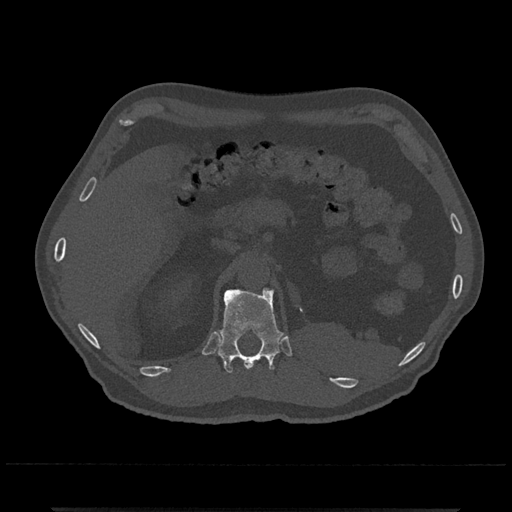
CT including the spine, one axial slice; slice 436 of 797 in the series (ordered by position); 120 kVp; bone window (W 1800 / L 400 HU); 0.5 mm slice thickness; 512 × 512 image matrix, field of view 393 × 393 mm. Patient: male, 67 years. Case-level facts recorded for this patient, not image findings: primary cancer: prostate.
Outlined on this slice (semi-automatic segmentation, software-assisted and operator-edited):
- T12 vertebra: bounding box <217,288,283,373> (left, top, right, bottom; pixels)